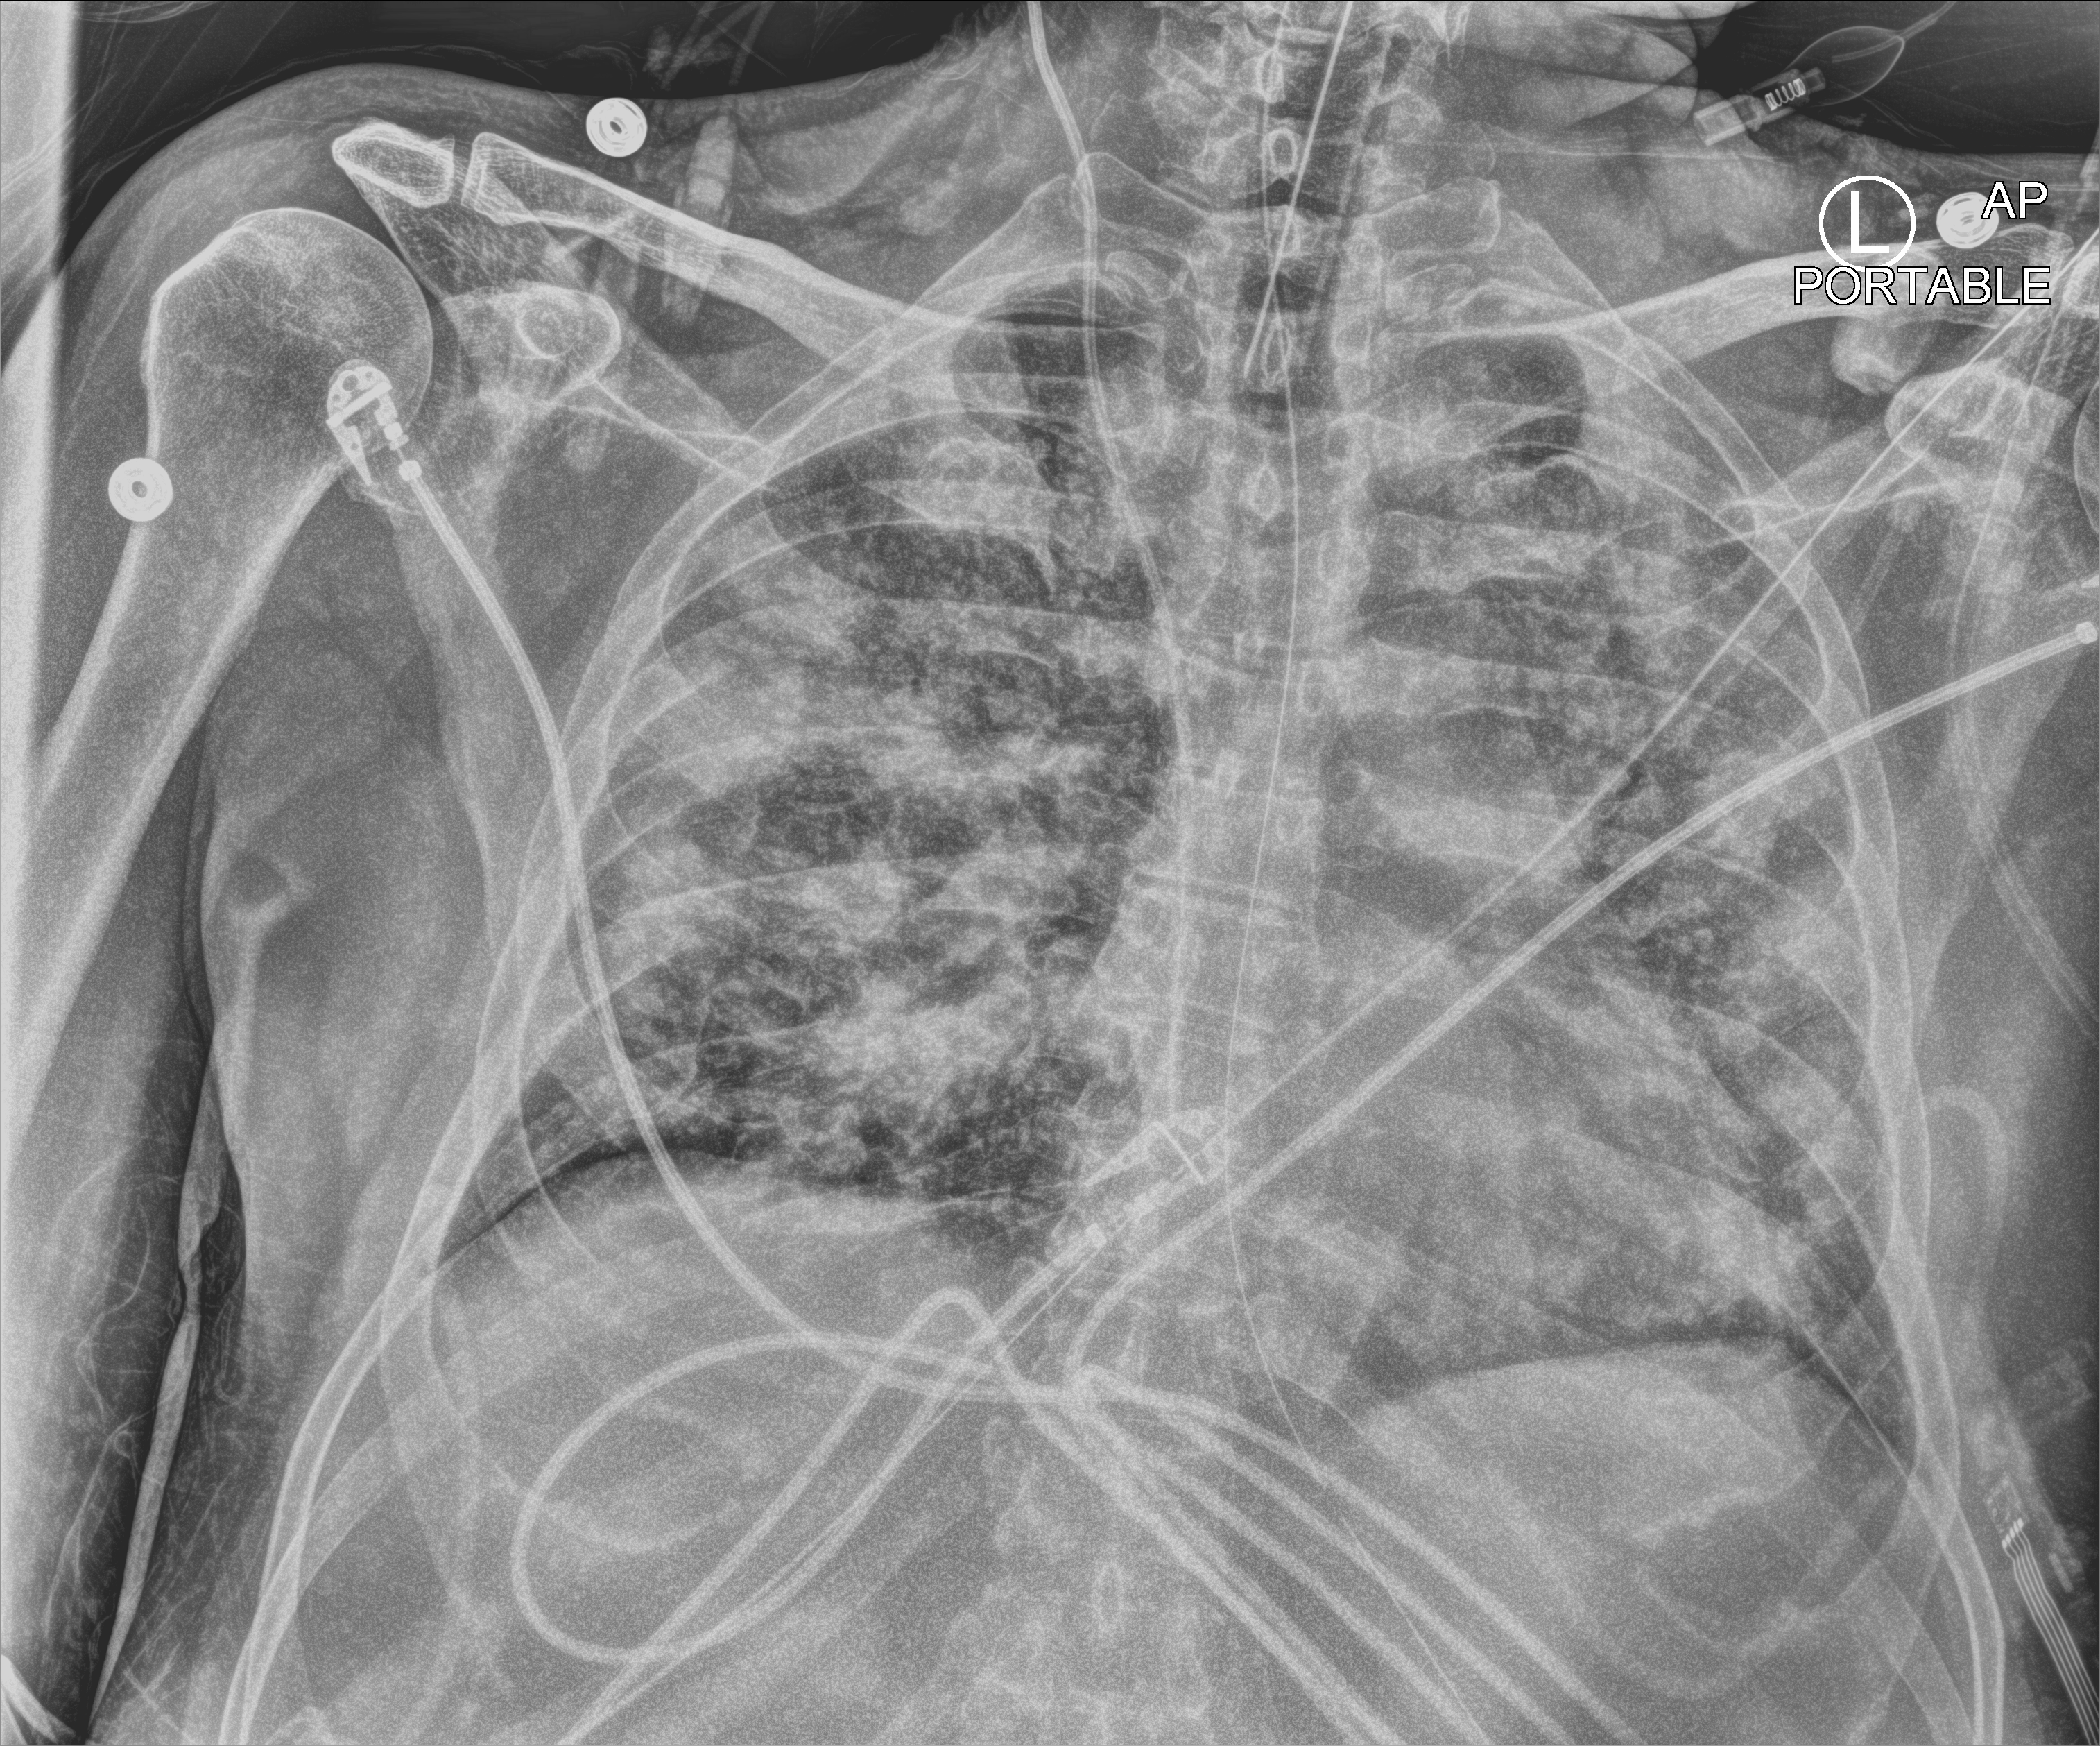
Chest X-ray (portable), anteroposterior (AP) projection. Male patient hospitalised with COVID-19, age 18–59 years.
Admission-level facts for this patient (not findings on this image; timing relative to this image not recorded): other chronic lung disease (admission record): no; admitted to intensive care during this hospital stay: yes; mechanically ventilated during this hospital stay: yes.